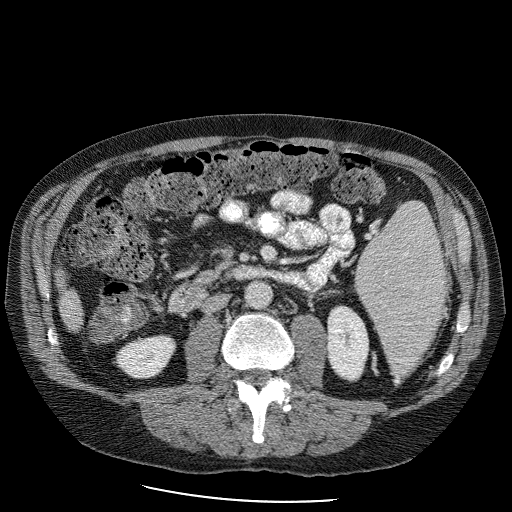
Contrast-enhanced abdominal CT (liver protocol), one axial slice. Slice 22 of 98 in the series (ordered by position). Reconstruction kernel STANDARD. 120 kVp. Soft-tissue window (W 400 / L 40 HU). 512 × 512 image matrix. From the clinical record (not read from this slice): diagnosis: hepatocellular carcinoma (patient treated with transarterial chemoembolisation; whether this scan precedes or follows treatment is not stated here); TNM stage (as recorded): Stage-II; Child-Pugh class: B; tumour differentiation: moderately differentiated; tumour nodularity: uninodular.
Annotated regions visible in this slice (semi-automatic segmentation, software-assisted and operator-edited):
- liver parenchyma outside the tumour (the mass and vessels are separate outlines, so this box may not span the whole liver): box from (x=52, y=243) to (x=82, y=332) px